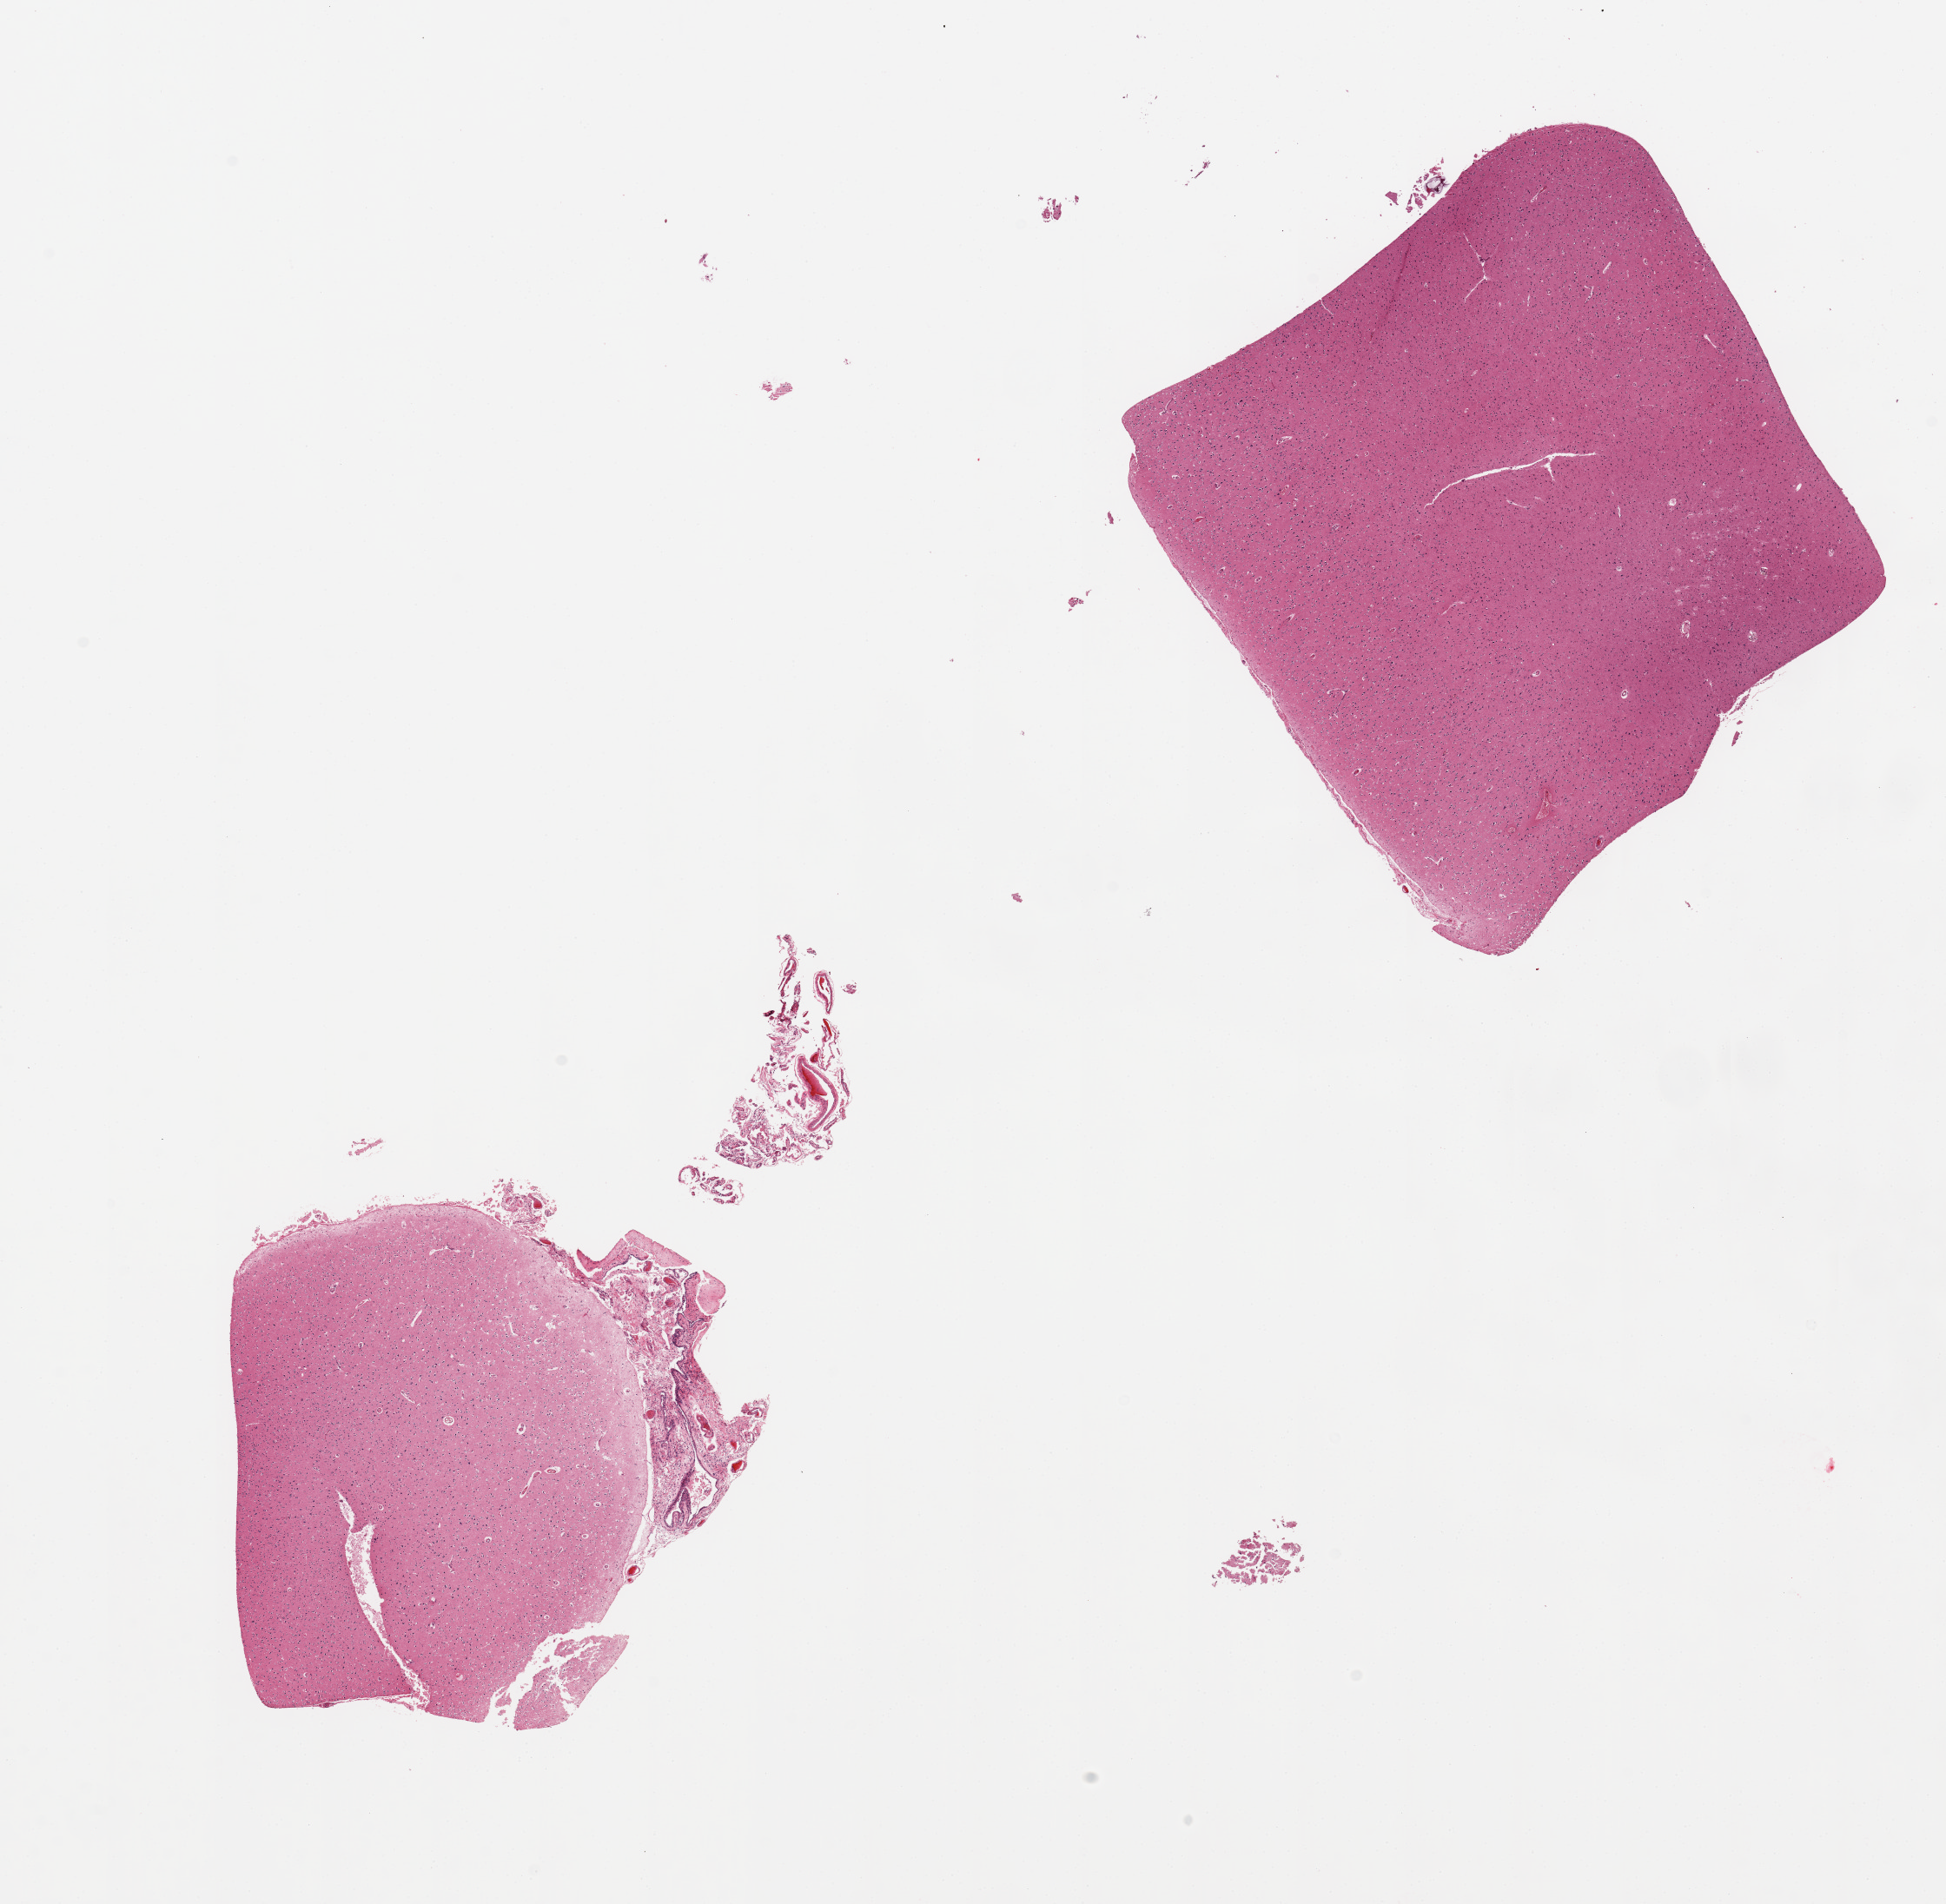
Haematoxylin and eosin whole-slide image, low-resolution overview of the scanned area, about 17.7 x 17.3 mm. PAXgene-fixed paraffin-embedded (PFPE) section. Target tissue: cerebral cortex. Donor tissue sample. Male donor.
• review note (as recorded): 2 pieces; adherent meninges on 1